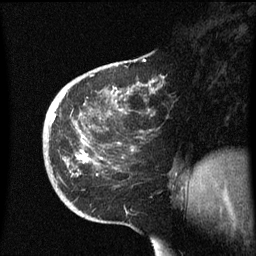
Breast MRI (dynamic contrast-enhanced), one sagittal slice. Slice 21 of 60 in the series (ordered by position). Dynamic contrast-enhanced series, image 2 of 3 at this slice position (ordered by acquisition). 1.5 T. TE 4.2 ms, TR 8.4 ms. 2.3 mm slice thickness. 256 × 256 image matrix, field of view 200 × 200 mm. Female patient, age 38 years. From the clinical record (not read from this slice): setting: breast cancer imaged before/during neoadjuvant chemotherapy; receptor status: HER2-positive.
Structures marked on this image (semi-automatic segmentation, software-assisted and operator-edited):
- analysis volume of interest (the breast-tissue region the enhancement analysis was run in; not a lesion): bounding box (x1, y1, x2, y2) in pixels: (43, 78, 191, 213)
- tumour enhancement mask (voxels above the 70 % enhancement threshold inside the analysis volume of interest): (52, 114, 90, 163)